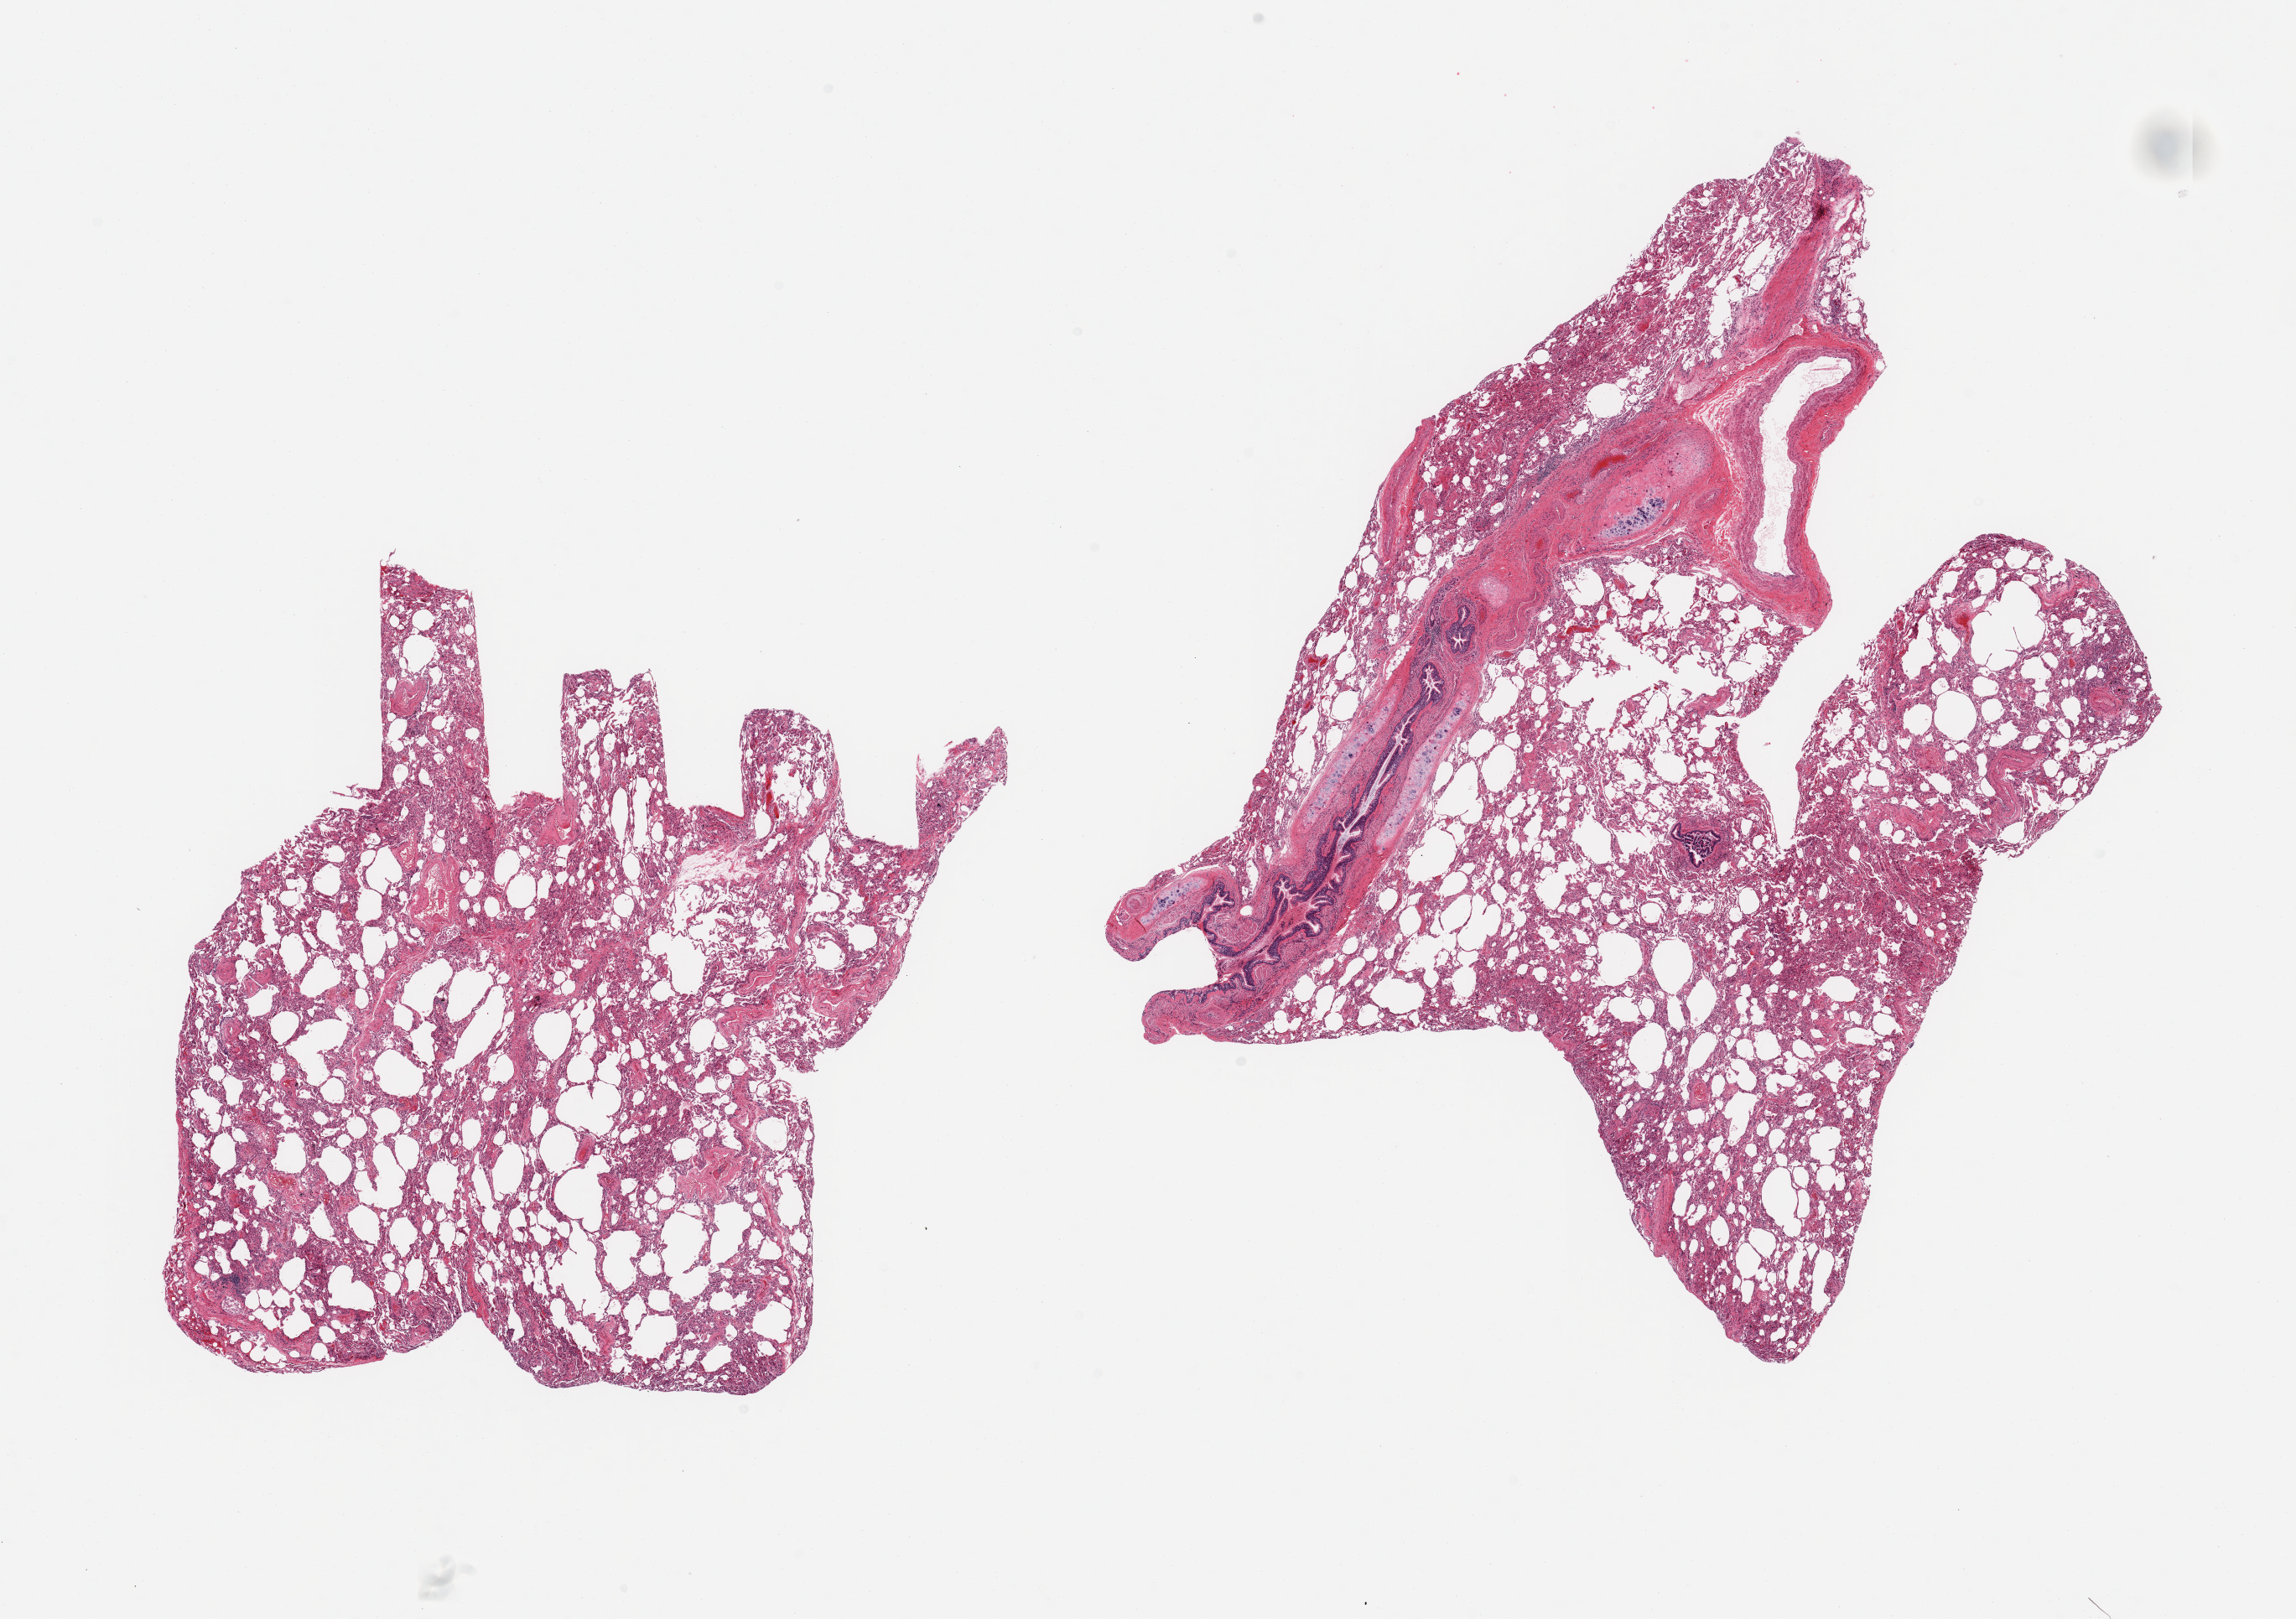
Digitized H&E-stained section, brightfield — whole scanned area (about 21.7 x 15.3 mm, from a 20x scan) shown as a low-resolution overview. PAXgene-fixed paraffin-embedded (PFPE) section. Section of lung (target tissue). Tissue donor sample. Donor: male.
Review note (as recorded): 2 pieces; one contains bronchus with cartilage and vessel; emphysematous and athelectatic changes; congestion.